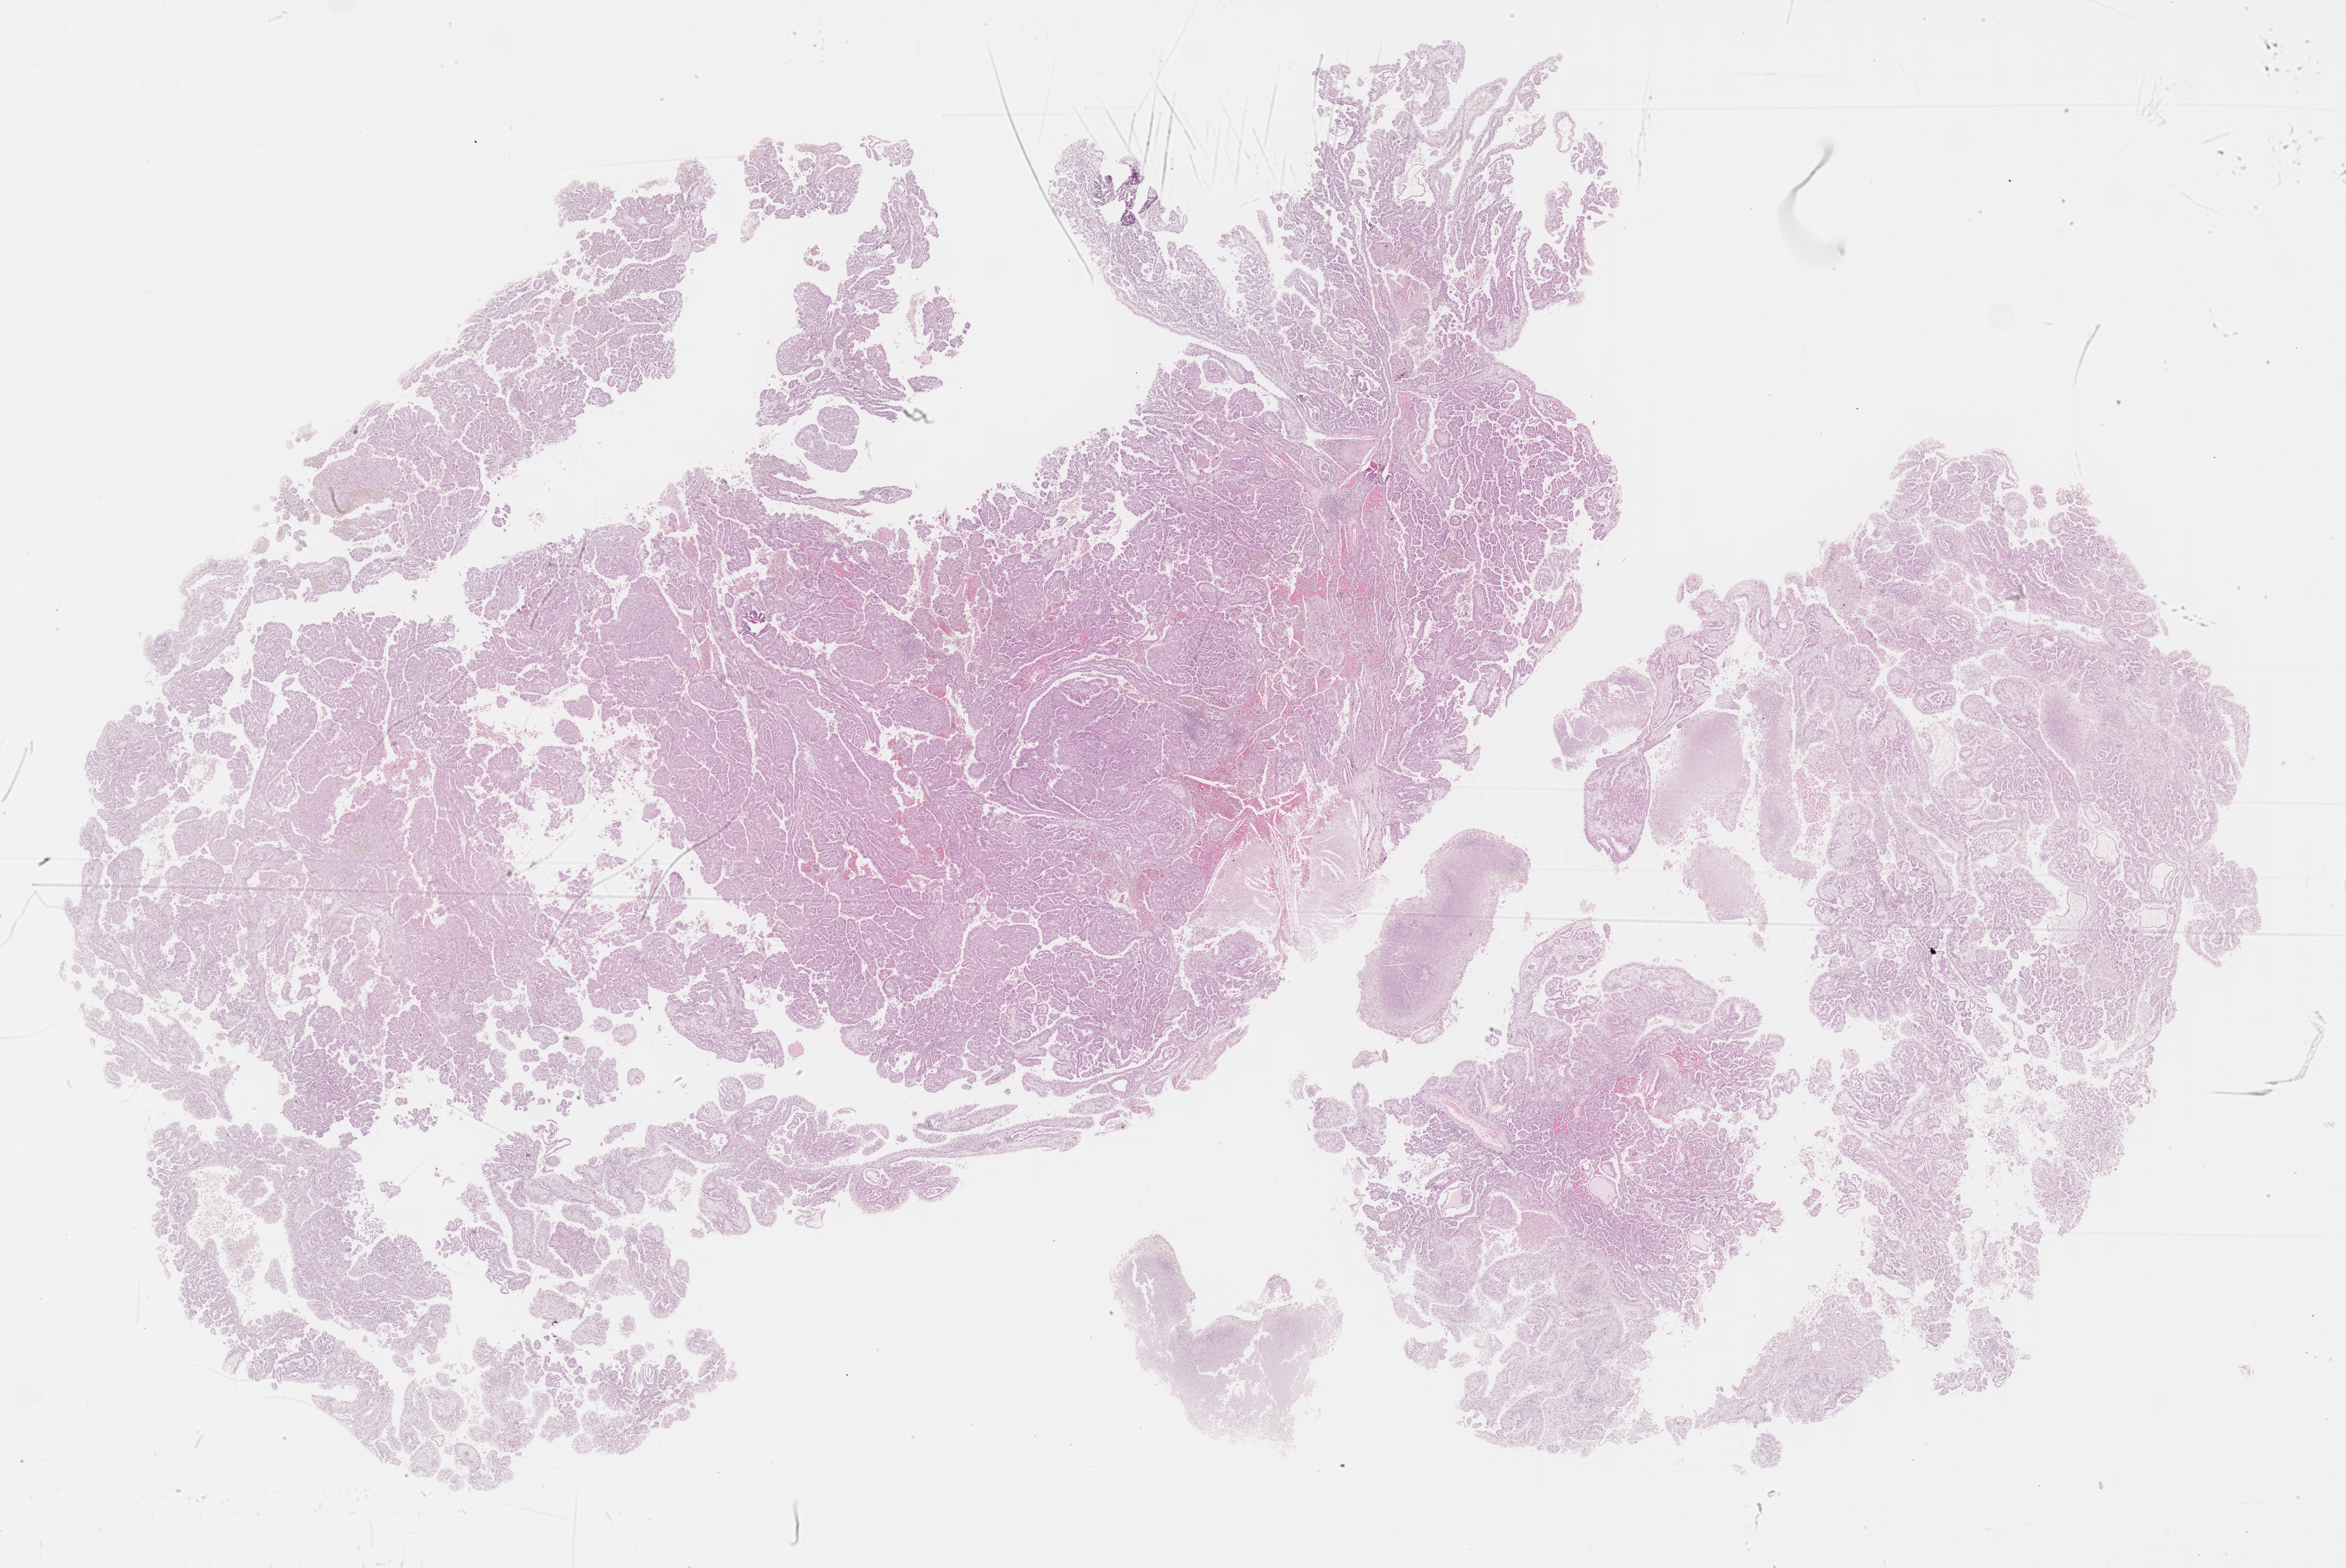
Digitized H&E-stained tissue section (whole slide) — whole scanned area (about 30.7 x 20.5 mm, from a 40x scan) shown as a low-resolution overview; formalin-fixed paraffin-embedded (FFPE) diagnostic section; primary tumour sample from the kidney. Patient: male, age at initial diagnosis 67 years.
Diagnosis: Papillary adenocarcinoma, NOS. Lymph nodes positive (case pathology): 1 of 3 examined. Laterality: left. AJCC pathologic stage: III (7th edition). TNM: T1b N1 MX.